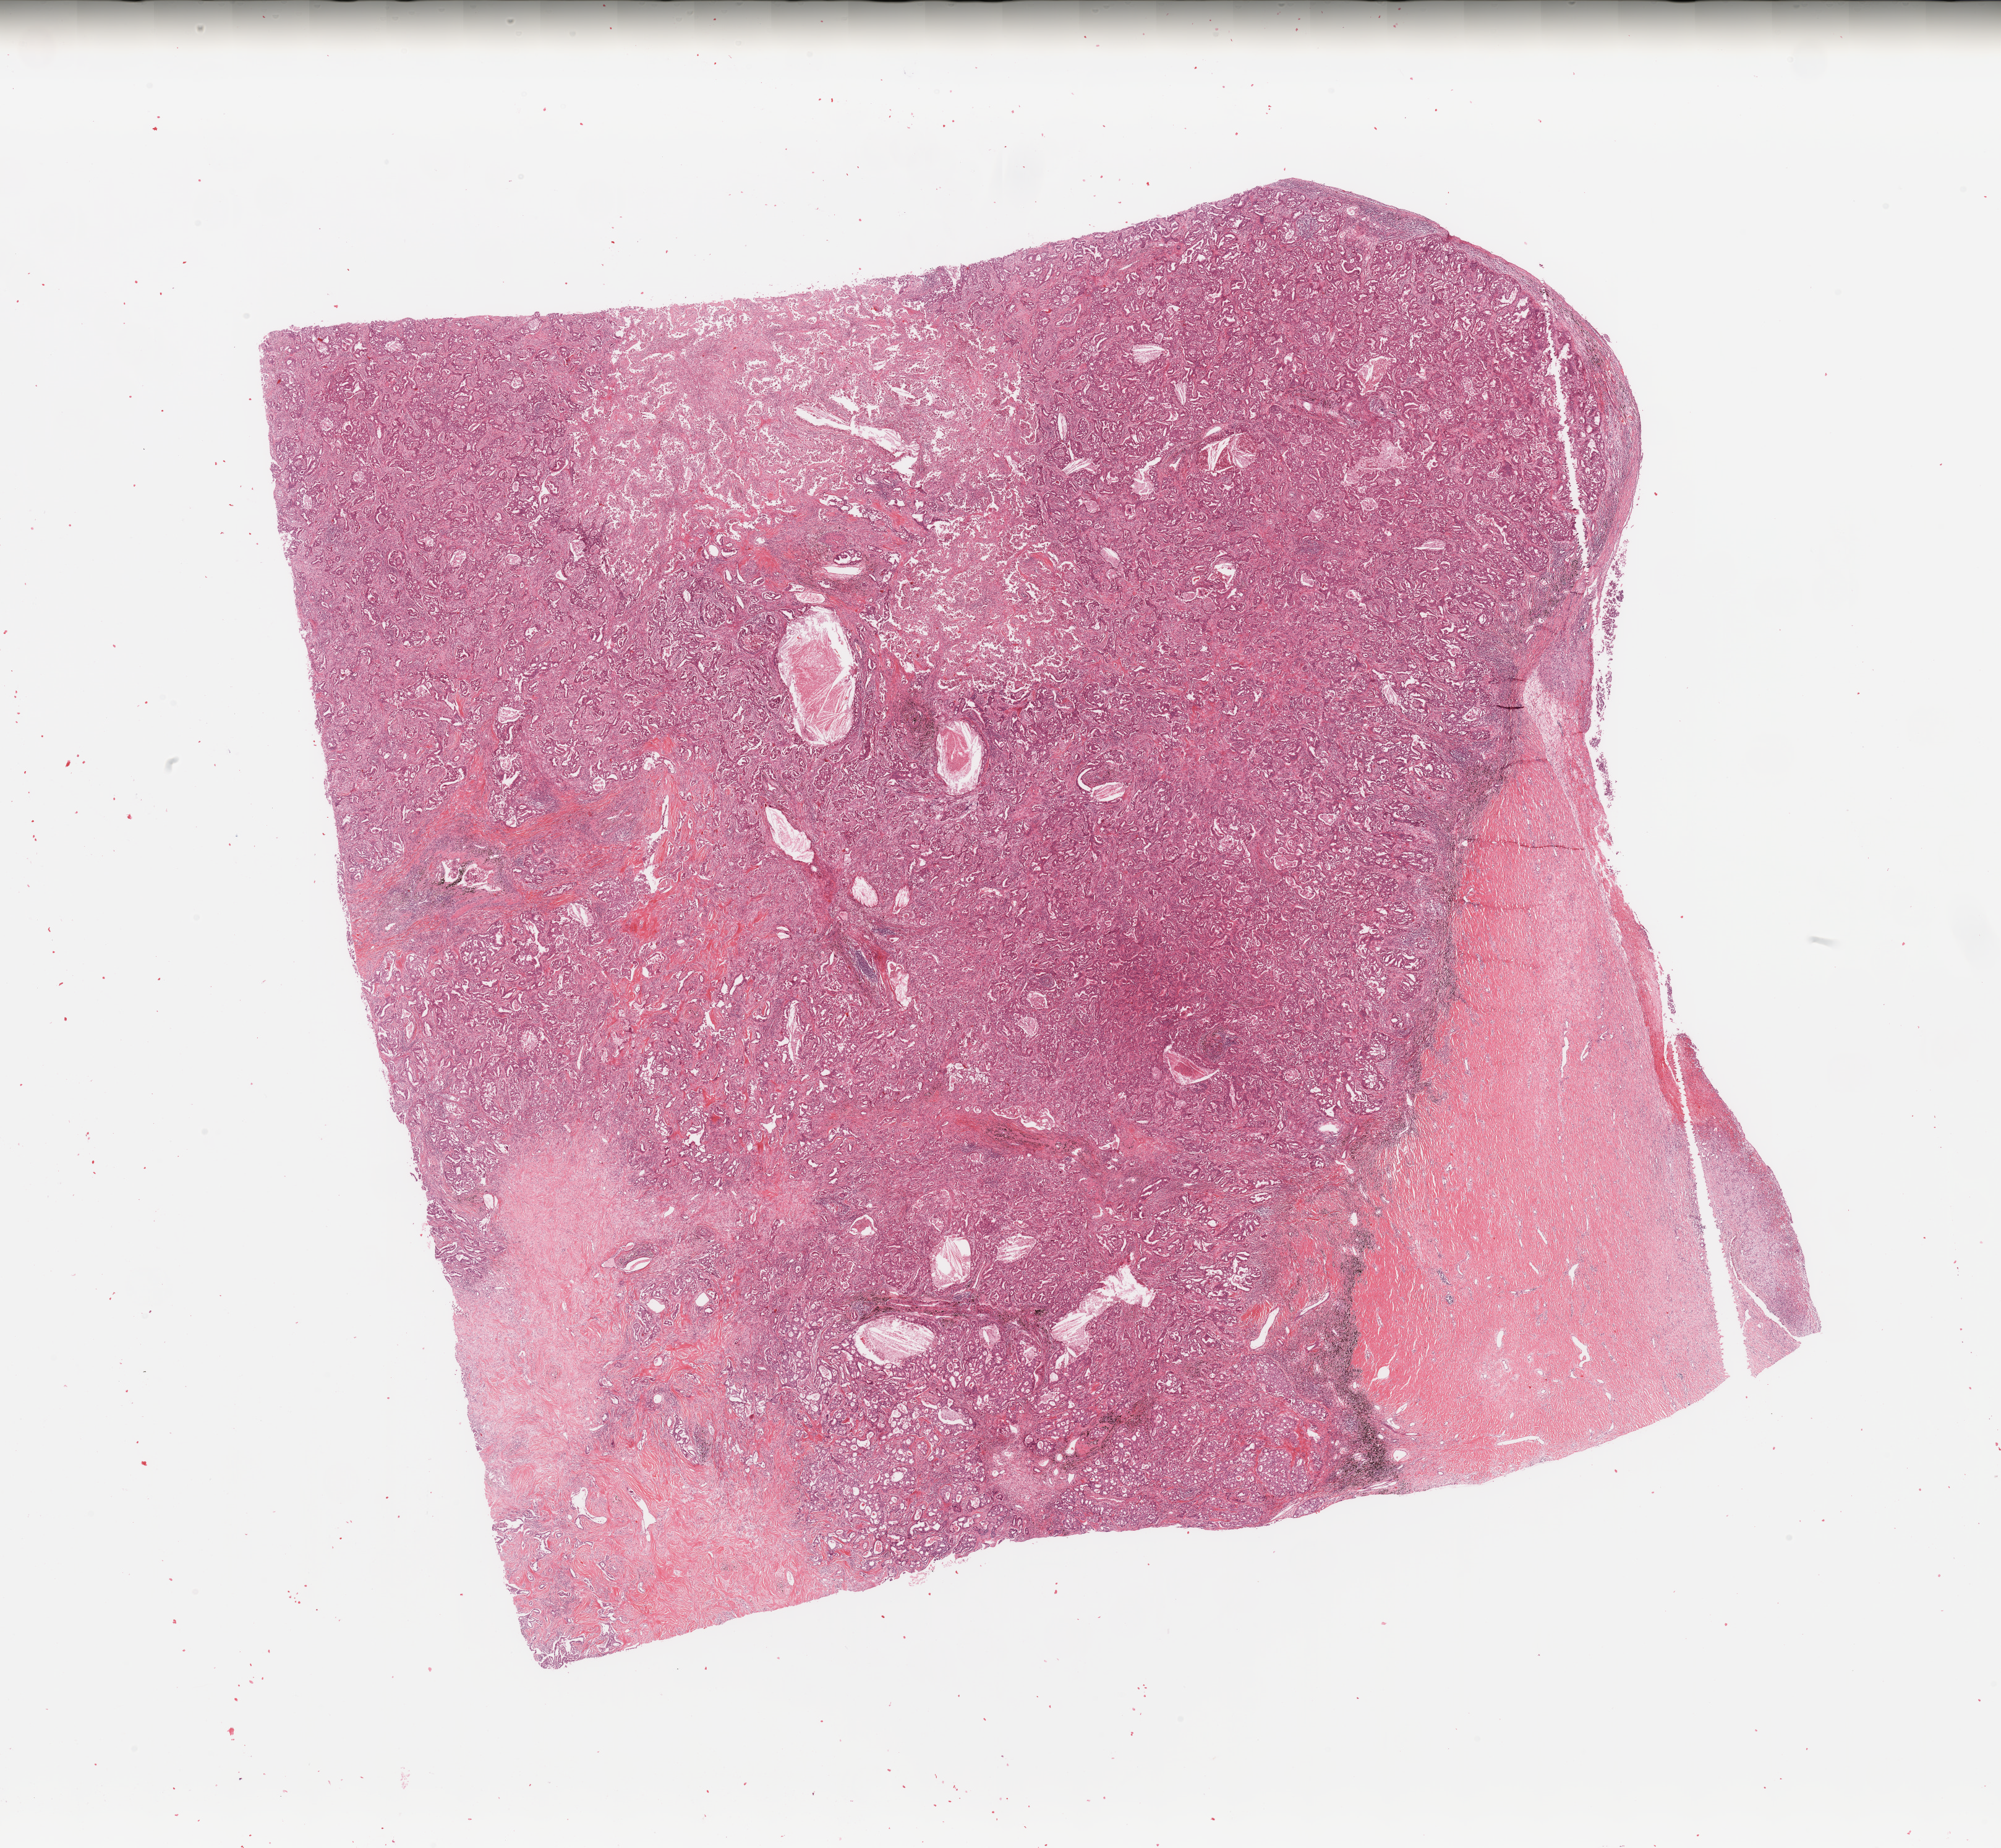
Whole-slide histology image, Hematoxylin and eosin (H&E) stained, low-resolution overview of the scanned area, about 25.6 x 23.6 mm (acquisition: 20x scan); lung, tumour tissue. 54-year-old female patient. Histologic grade: G2 (moderately differentiated).
AJCC pathologic stage: IIIA. Diagnosis: Adenocarcinoma, NOS.